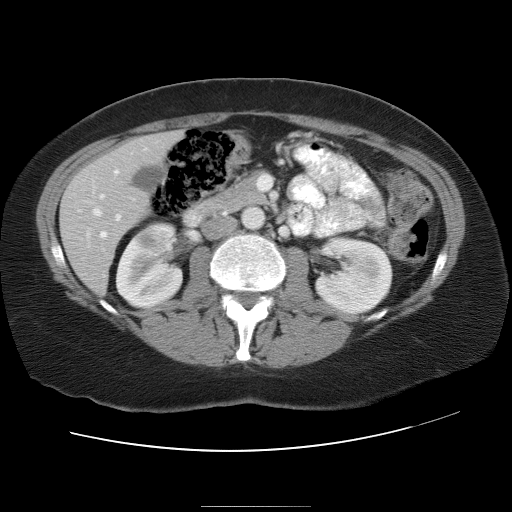
Contrast-enhanced abdominal CT, one axial slice; position 13 of 30 along the scan axis; 120 kVp; intravenous contrast given; soft-tissue window (W 400 / L 40 HU); 7.5 mm slice thickness; 512 × 512 image matrix, field of view 376 × 376 mm. Female patient, age 52 years. Case-level facts recorded for this patient, not image findings: diagnosis: colorectal cancer liver metastases, imaged before liver resection; multiple liver metastases: no; largest metastasis: 3 cm.
Structures marked on this image (manually delineated by an expert):
- hepatic veins: box from (x=93, y=209) to (x=100, y=216) px
- liver: (x=61, y=131)–(x=183, y=292)
- planned liver remnant (the part of the liver to remain after resection): (x=164, y=131)–(x=184, y=146)
- portal vein (with intrahepatic branches): (x=100, y=170)–(x=133, y=238)